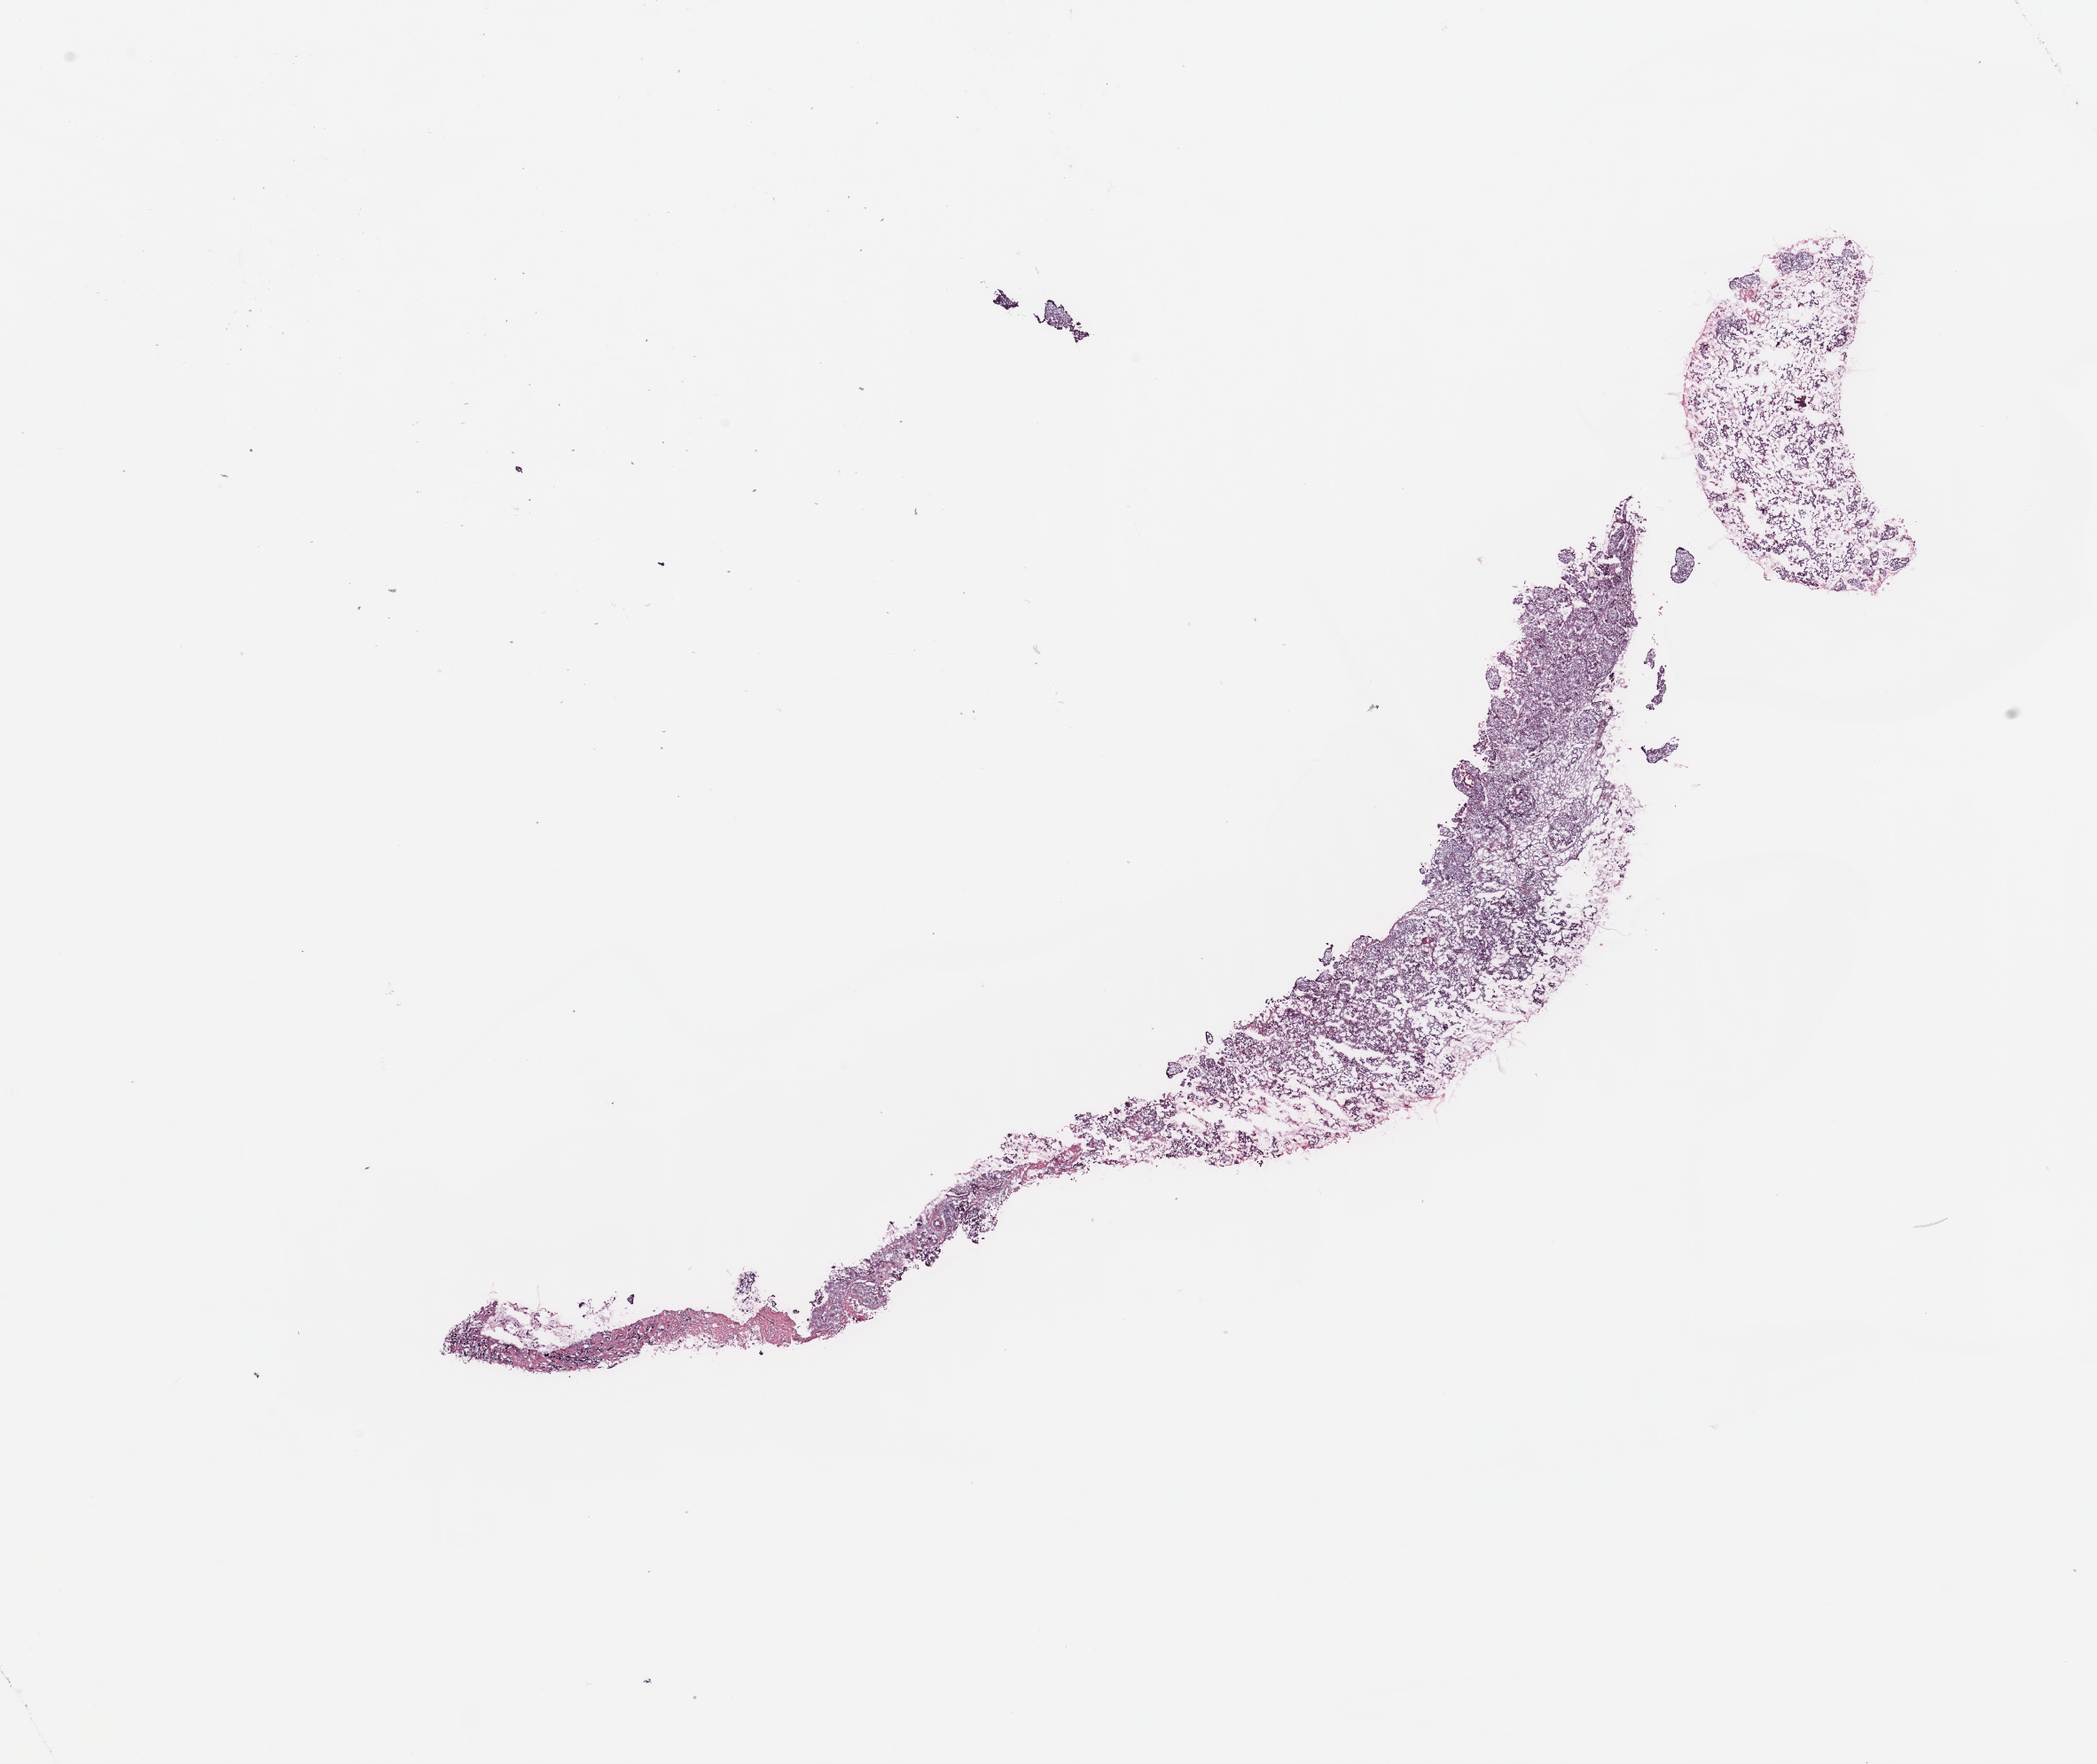
Whole-slide histology image, Hematoxylin and eosin (H&E) stained, a low-resolution overview of the entire scanned area, about 18.7 x 15.7 mm; tumour tissue sample, breast. Female, 62 y/o.
AJCC pathologic stage: IIIA. Diagnosis: Infiltrating duct carcinoma, NOS.